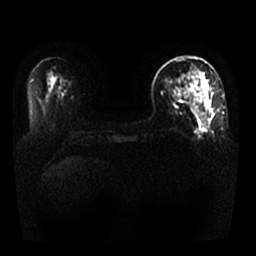
Breast MRI, one axial slice; position 12 of 25 along the scan axis; diffusion-weighted series; image 2 of 4 stored at this slice position (different b-values; order by instance number); 1.5 T; 4 mm slice thickness; 256 × 256 image matrix, field of view 330 × 330 mm. Female patient.
Outlined on this slice (outlined manually by an expert reader):
- tumour on diffusion-weighted imaging: bounding box [x1, y1, x2, y2] px = [206, 101, 209, 107]